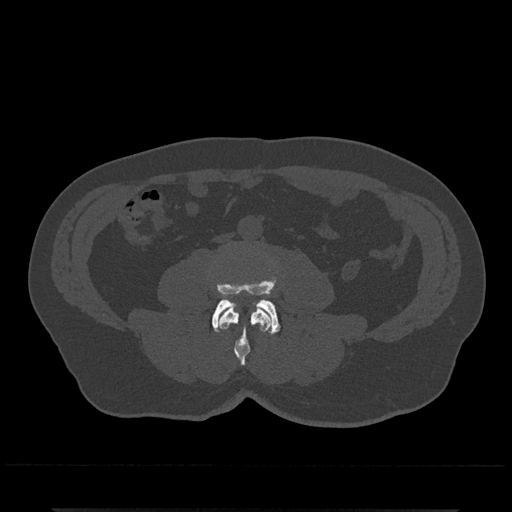
CT including the spine, one axial slice; slice 187 of 797 in the series (ordered by position); reconstruction kernel Br40s/3; 120 kVp; bone window (W 1800 / L 400 HU); 0.5 mm slice thickness; 512 × 512 image matrix. Male patient, age 67 years. Case-level facts recorded for this patient, not image findings: primary cancer: prostate.
Outlined on this slice (semi-automatic segmentation, software-assisted and operator-edited):
- L3 vertebra: bounding box (x1, y1, x2, y2) in pixels: (218, 306, 272, 365)
- L4 vertebra: (212, 280, 280, 334)